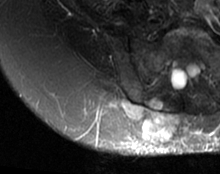
MRI of an extremity soft-tissue mass, one axial slice; position 45 of 63 along the scan axis; T2-weighted fat-saturated; MR volume resampled by the dataset authors to the PET/CT grid (not the native acquisition matrix); 3.27 mm slice thickness; 220 × 174 image matrix, field of view 215 × 170 mm. Female patient. Case-level facts recorded for this patient, not image findings: histological type: spindle cell suggestive of myxofibrosarcoma; grade: intermediate; site of the primary tumour: right buttock.
Outlined on this slice (expert contour drawn on MRI and transferred to this co-registered scan by the dataset authors):
- gross tumour volume (mass): bounding box <109,98,178,142> (left, top, right, bottom; pixels)